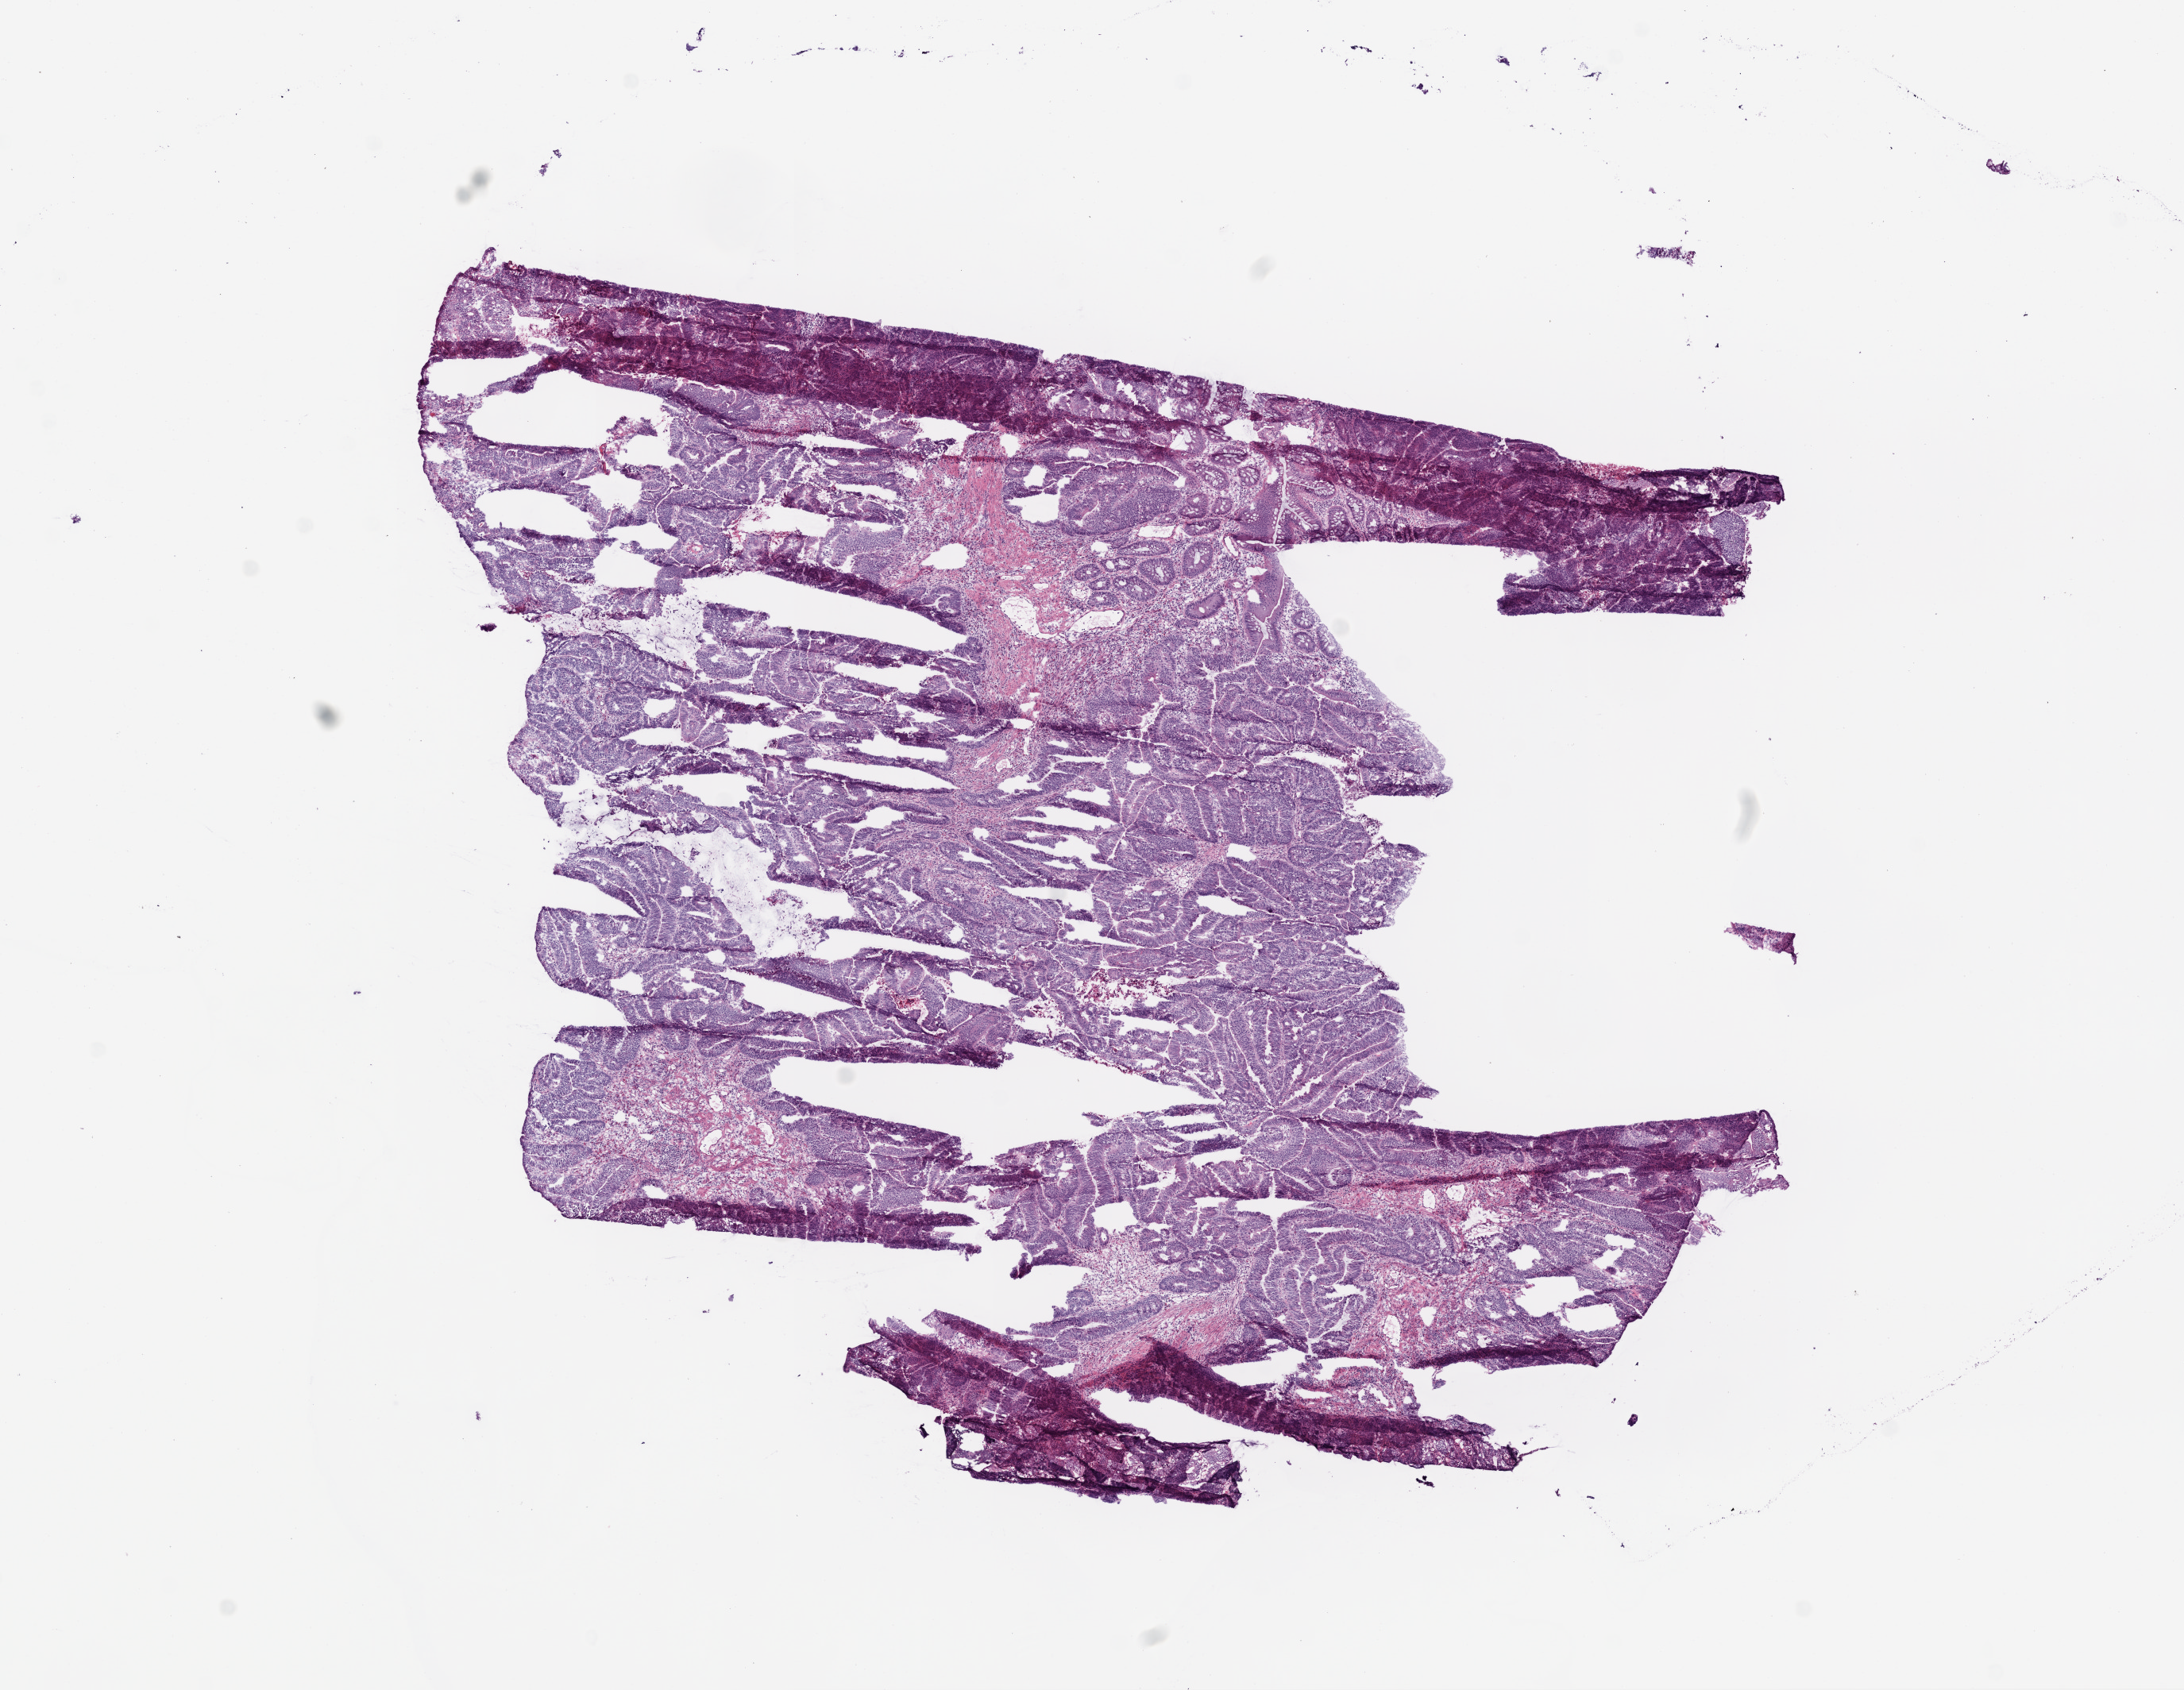
Whole-slide histology image, H&E-stained — whole scanned area (about 11.0 x 8.5 mm, from a 20x scan) shown as a low-resolution overview; frozen section from the bottom of the tissue portion; primary tumour sample from the rectum. Male, age 70 years at initial diagnosis. Slide review estimates, as recorded: tumour cells 80%, tumour nuclei 80%, normal cells 15%, stromal cells 5%, necrosis 0%.
- lymph nodes positive (case pathology): 0 of 12 examined
- diagnosis: Mucinous adenocarcinoma (rectosigmoid junction)
- AJCC pathologic stage: I (5th edition)